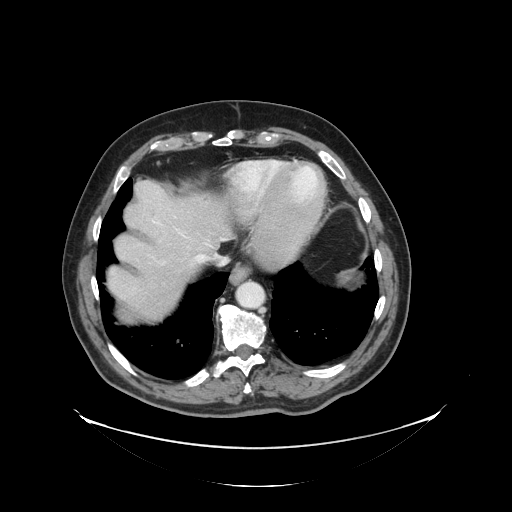
Contrast-enhanced abdominal CT, one axial slice. Slice 117 of 138 in the series (ordered by position). Reconstruction kernel STANDARD. Soft-tissue window (W 400 / L 40 HU). 2.5 mm slice thickness. 512 × 512 image matrix, field of view 497 × 497 mm. Male patient, age 77 years. Case-level facts recorded for this patient, not image findings: diagnosis: colorectal cancer liver metastases, imaged before liver resection; multiple liver metastases: no.
Annotated regions visible in this slice (outlined manually by an expert reader):
- hepatic veins: bounding box [x1, y1, x2, y2] px = [162, 238, 225, 264]
- liver: [108, 182, 230, 321]
- planned liver remnant (the part of the liver to remain after resection): [108, 182, 230, 290]
- liver metastasis: [187, 273, 200, 286]